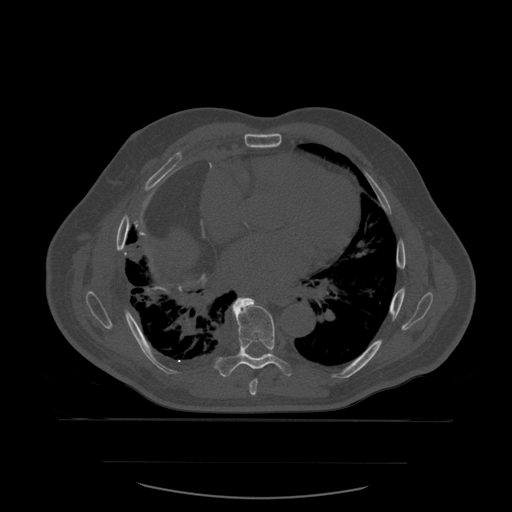
CT including the spine, one axial slice; bone window (W 1800 / L 400 HU); 1.25 mm slice thickness; 512 × 512 image matrix, field of view 479 × 479 mm. Patient age 71 years. Case-level facts recorded for this patient, not image findings: primary cancer: lung.
Structures marked on this image (semi-automatic segmentation, software-assisted and operator-edited):
- T7 vertebra: bounding box [x1, y1, x2, y2] px = [249, 379, 258, 396]
- T8 vertebra: [217, 297, 292, 377]